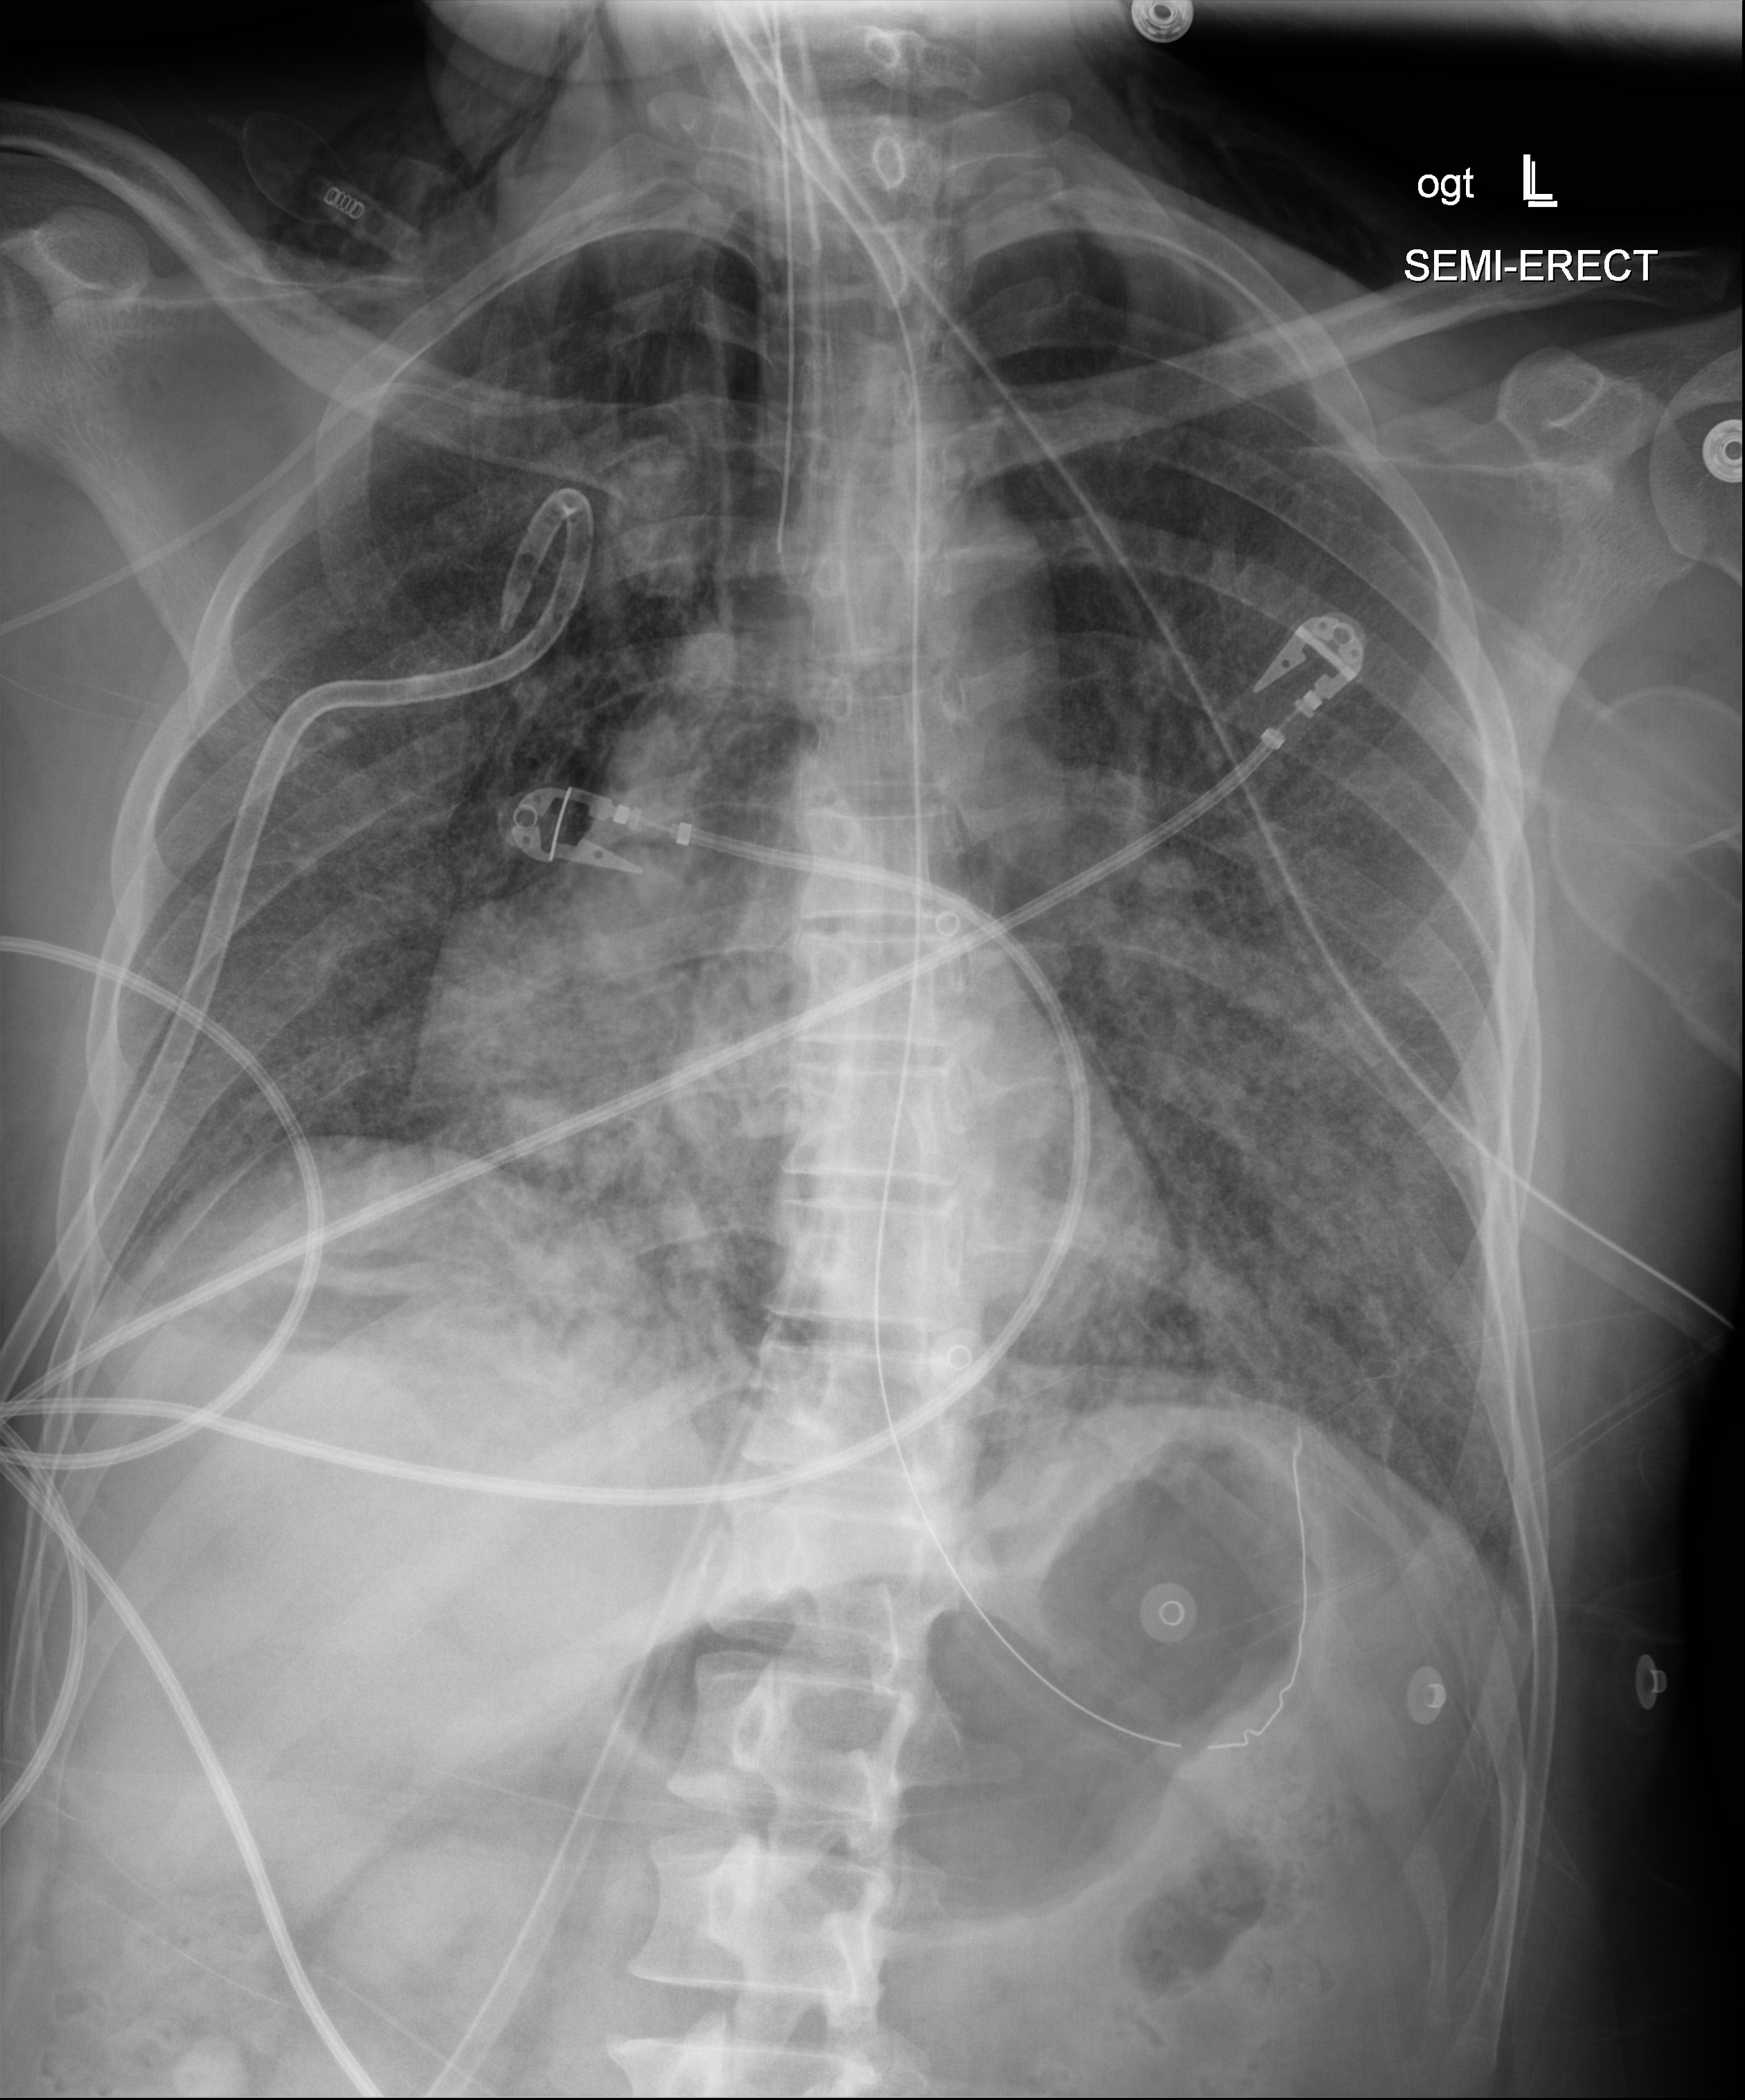
Chest X-ray (portable). Adult patient hospitalised with COVID-19, age 18–59 years.
From the hospital-stay record, not from the radiograph (when in the stay this image was taken is not recorded):
- admitted to intensive care during this hospital stay: yes